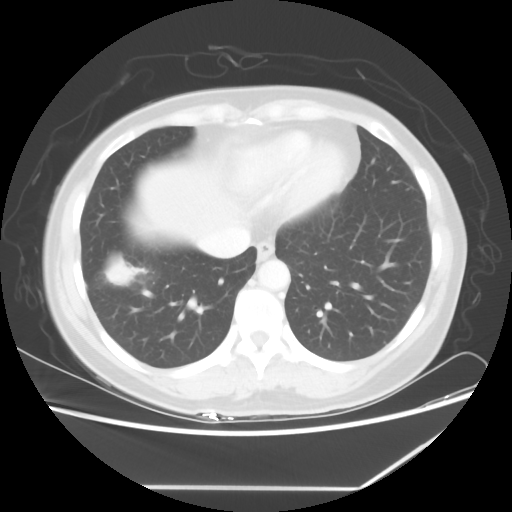
Chest CT, one axial slice. Position 20 of 60 along the scan axis. Reconstruction kernel STANDARD. Lung window (W 1500 / L -600 HU). 5 mm slice thickness. 512 × 512 image matrix, field of view 374 × 374 mm. Female patient, age 42 years. From the clinical record (not read from this slice): clinical TNM (as recorded): T2 N1 M0.
Annotated regions visible in this slice (bounding box drawn by a radiologist):
- lung tumour (recorded histology: adenocarcinoma): bounding box (x1, y1, x2, y2) in pixels: (103, 256, 159, 292)